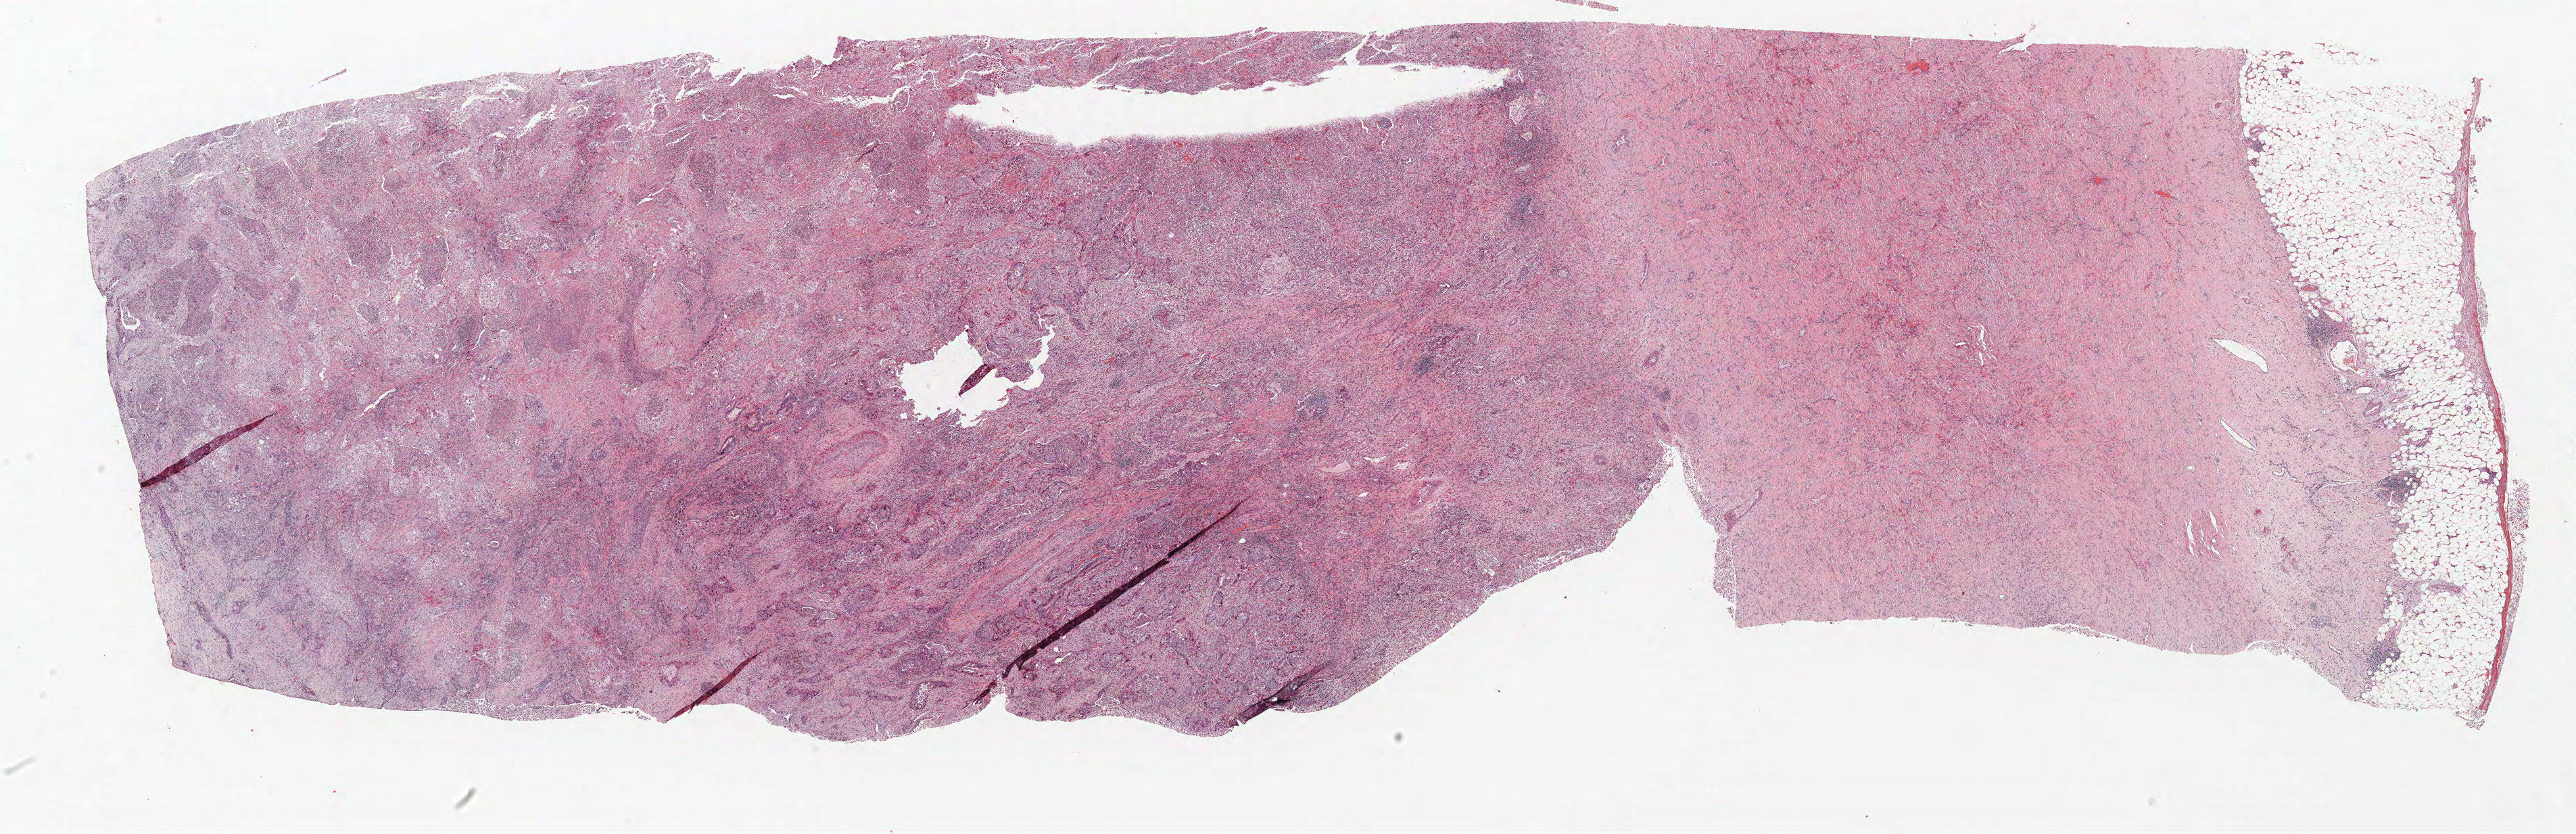
H&E-stained whole-slide image, low-resolution overview of the scanned area, about 30.5 x 9.9 mm (from a 40x scan), formalin-fixed paraffin-embedded (FFPE) section, lung. Male, age 63 at enrolment. Former smoker at enrolment. Grade: moderately differentiated (G2).
- participant's lung-cancer diagnosis: Squamous cell carcinoma, NOS (ICD-O-3 8070/3)
- tumour size (pathology): 80 mm
- primary tumour location (clinical record): right upper lobe
- stage (AJCC 6th edition): IB